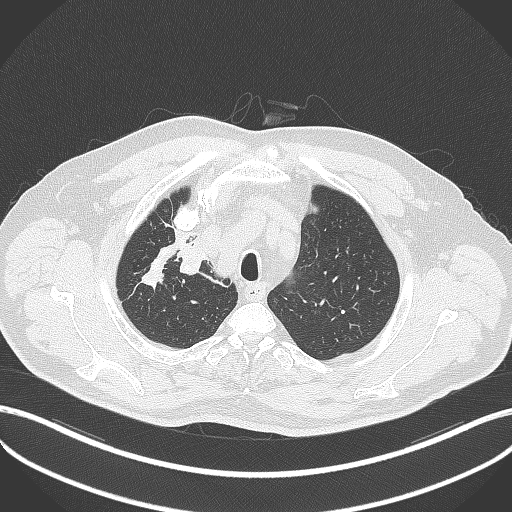
Chest CT, one axial slice. Position 321 of 411 along the scan axis. 120 kVp. Lung window (W 1500 / L -600 HU). 1 mm slice thickness. 512 × 512 image matrix. Patient: male, 60 years. Case-level facts recorded for this patient, not image findings: clinical TNM (as recorded): T1b N1 M0.
Structures marked on this image (bounding box drawn by a radiologist):
- lung tumour (recorded histology: squamous cell carcinoma): bounding box (x1, y1, x2, y2) in pixels: (176, 232, 212, 281)